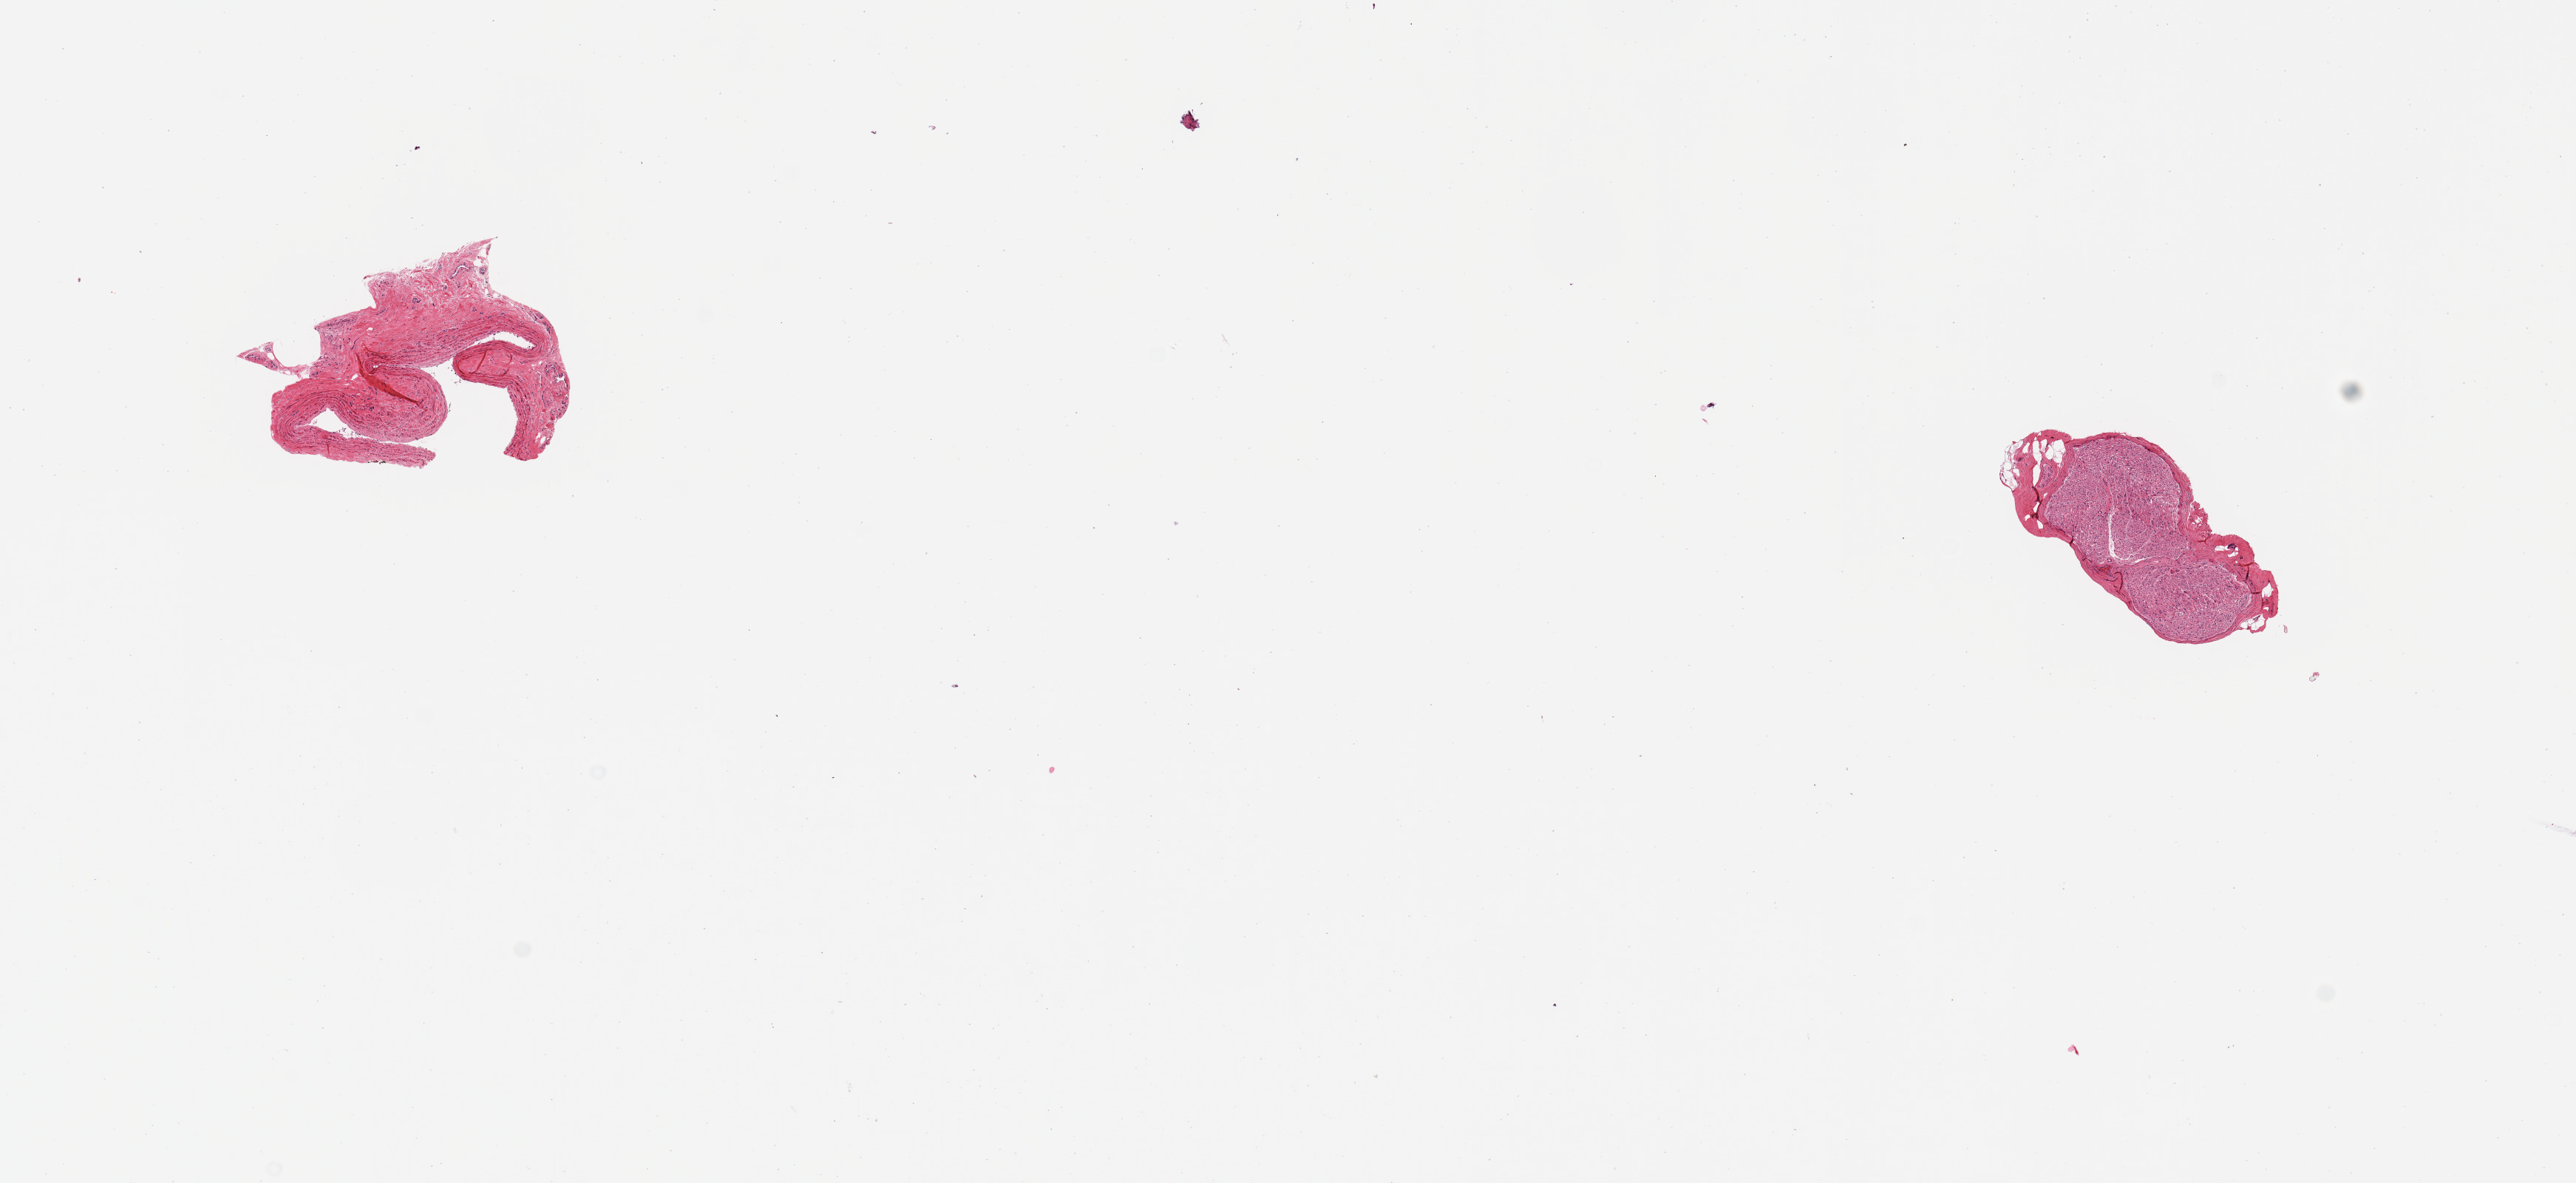
Digitized haematoxylin and eosin-stained section — whole scanned area (about 13.8 x 6.3 mm) shown as a low-resolution overview; PAXgene-fixed paraffin-embedded (PFPE) section; section of tibial artery (target tissue); donor tissue sample. Donor sex: female.
Pathologist's review note for this sample: 2 pieces; one piece is artery, one is nerve.